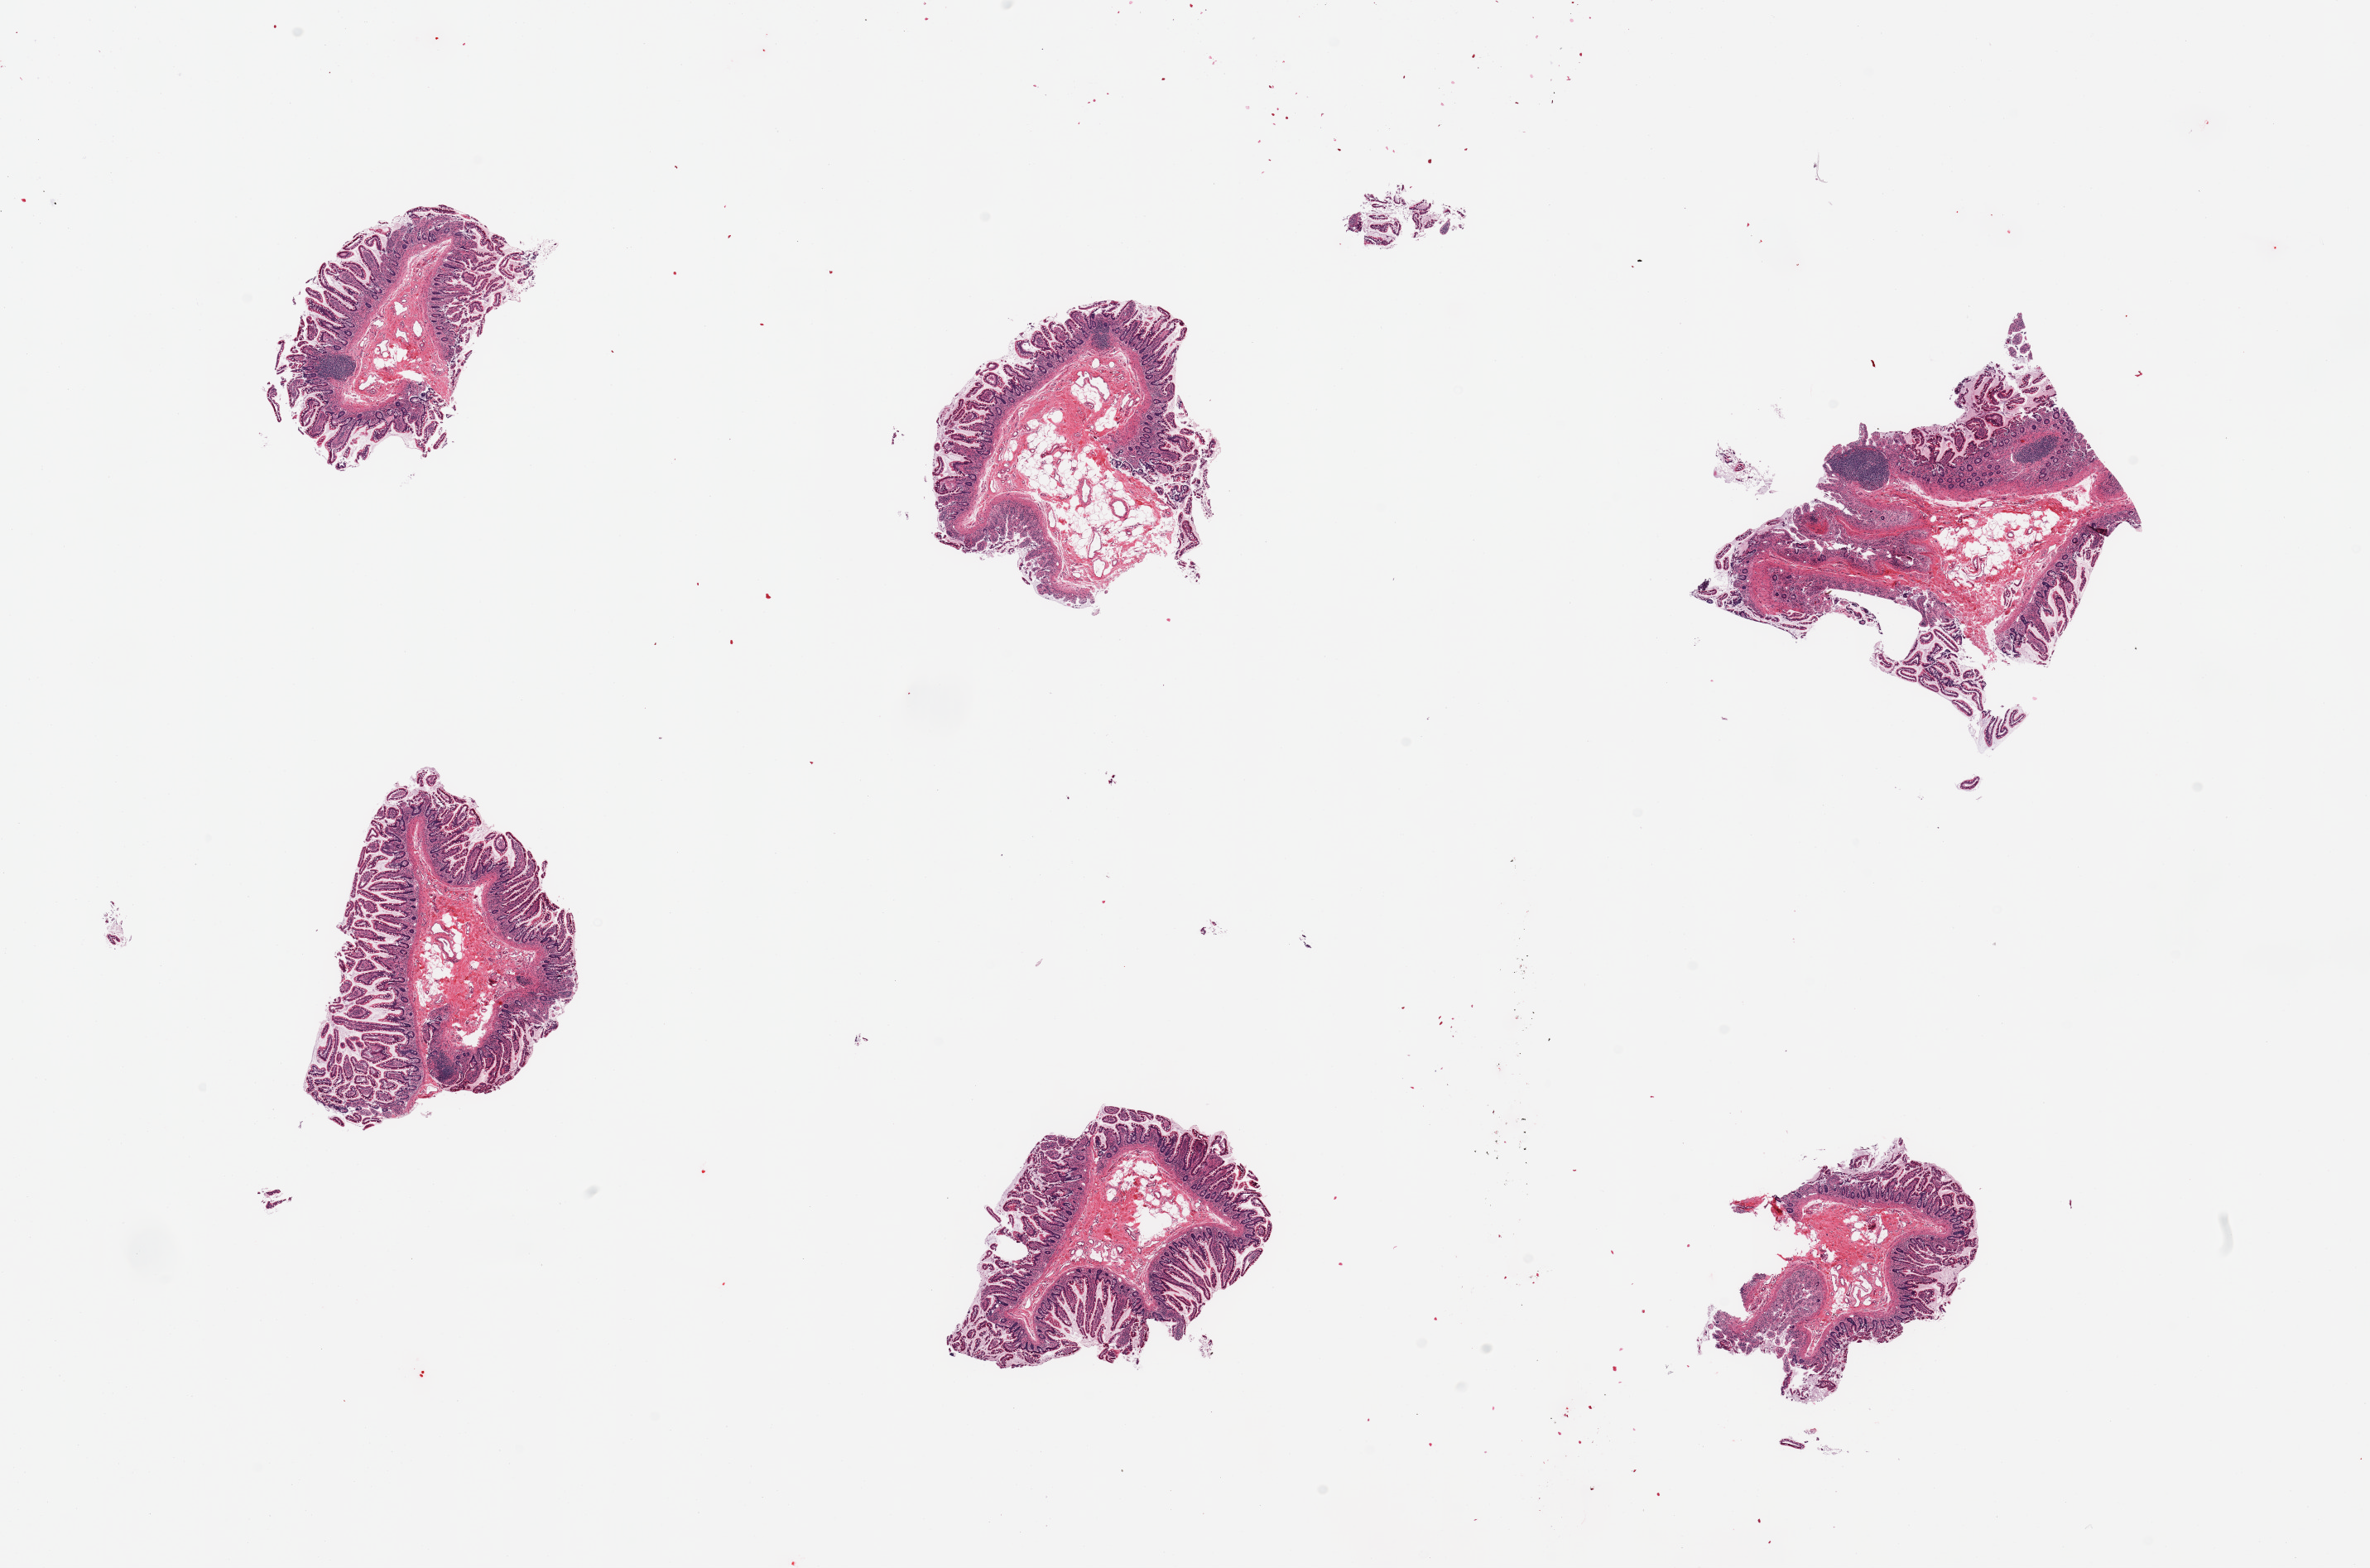
H&E whole-slide image — a low-resolution overview of the entire scanned area, about 22.6 x 15.0 mm; PAXgene-fixed, paraffin-embedded tissue; sampled site (target tissue): ileum; donor tissue sample.
- reviewer comment on this tissue sample: 6 pieces; mucosa with insufficient lymphoid tissue to warrant analysis